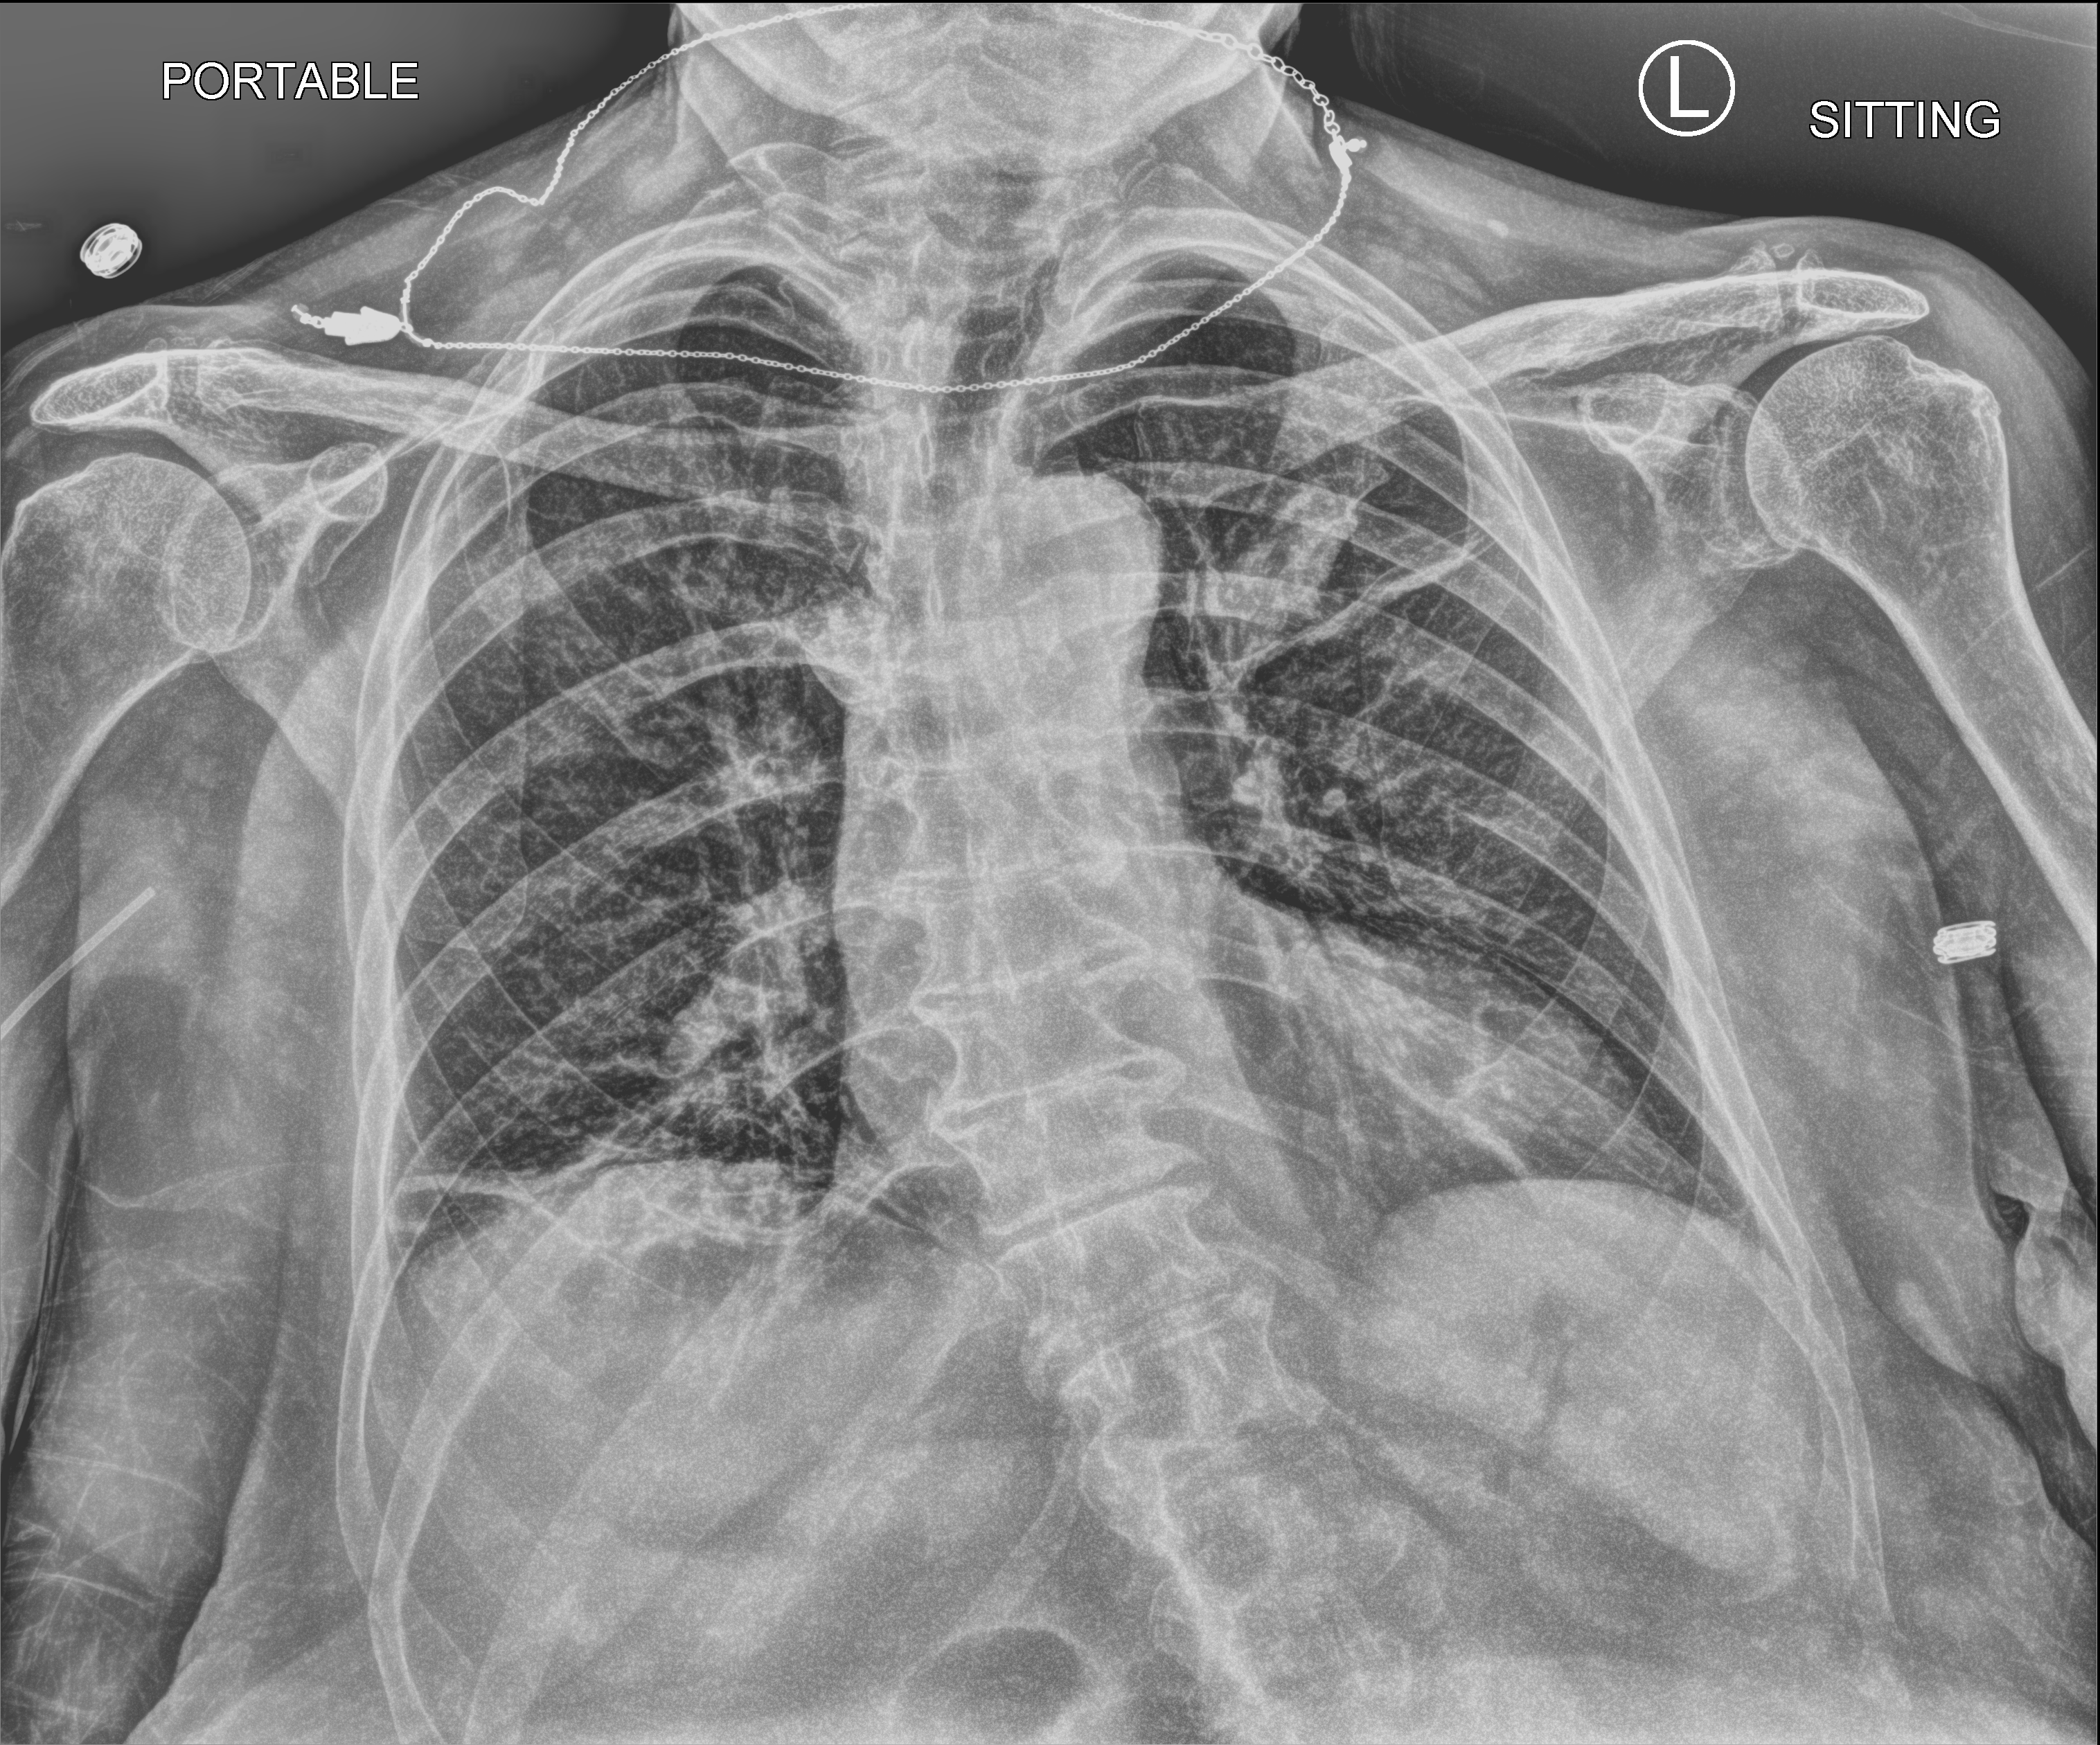
Bedside chest radiograph (computed radiography). Patient hospitalised with COVID-19; female, aged 60–74 years.
From the hospital-stay record, not from the radiograph (when in the stay this image was taken is not recorded):
- length of hospital stay: 16 days
- mechanically ventilated during this hospital stay: no
- admitted to intensive care during this hospital stay: yes